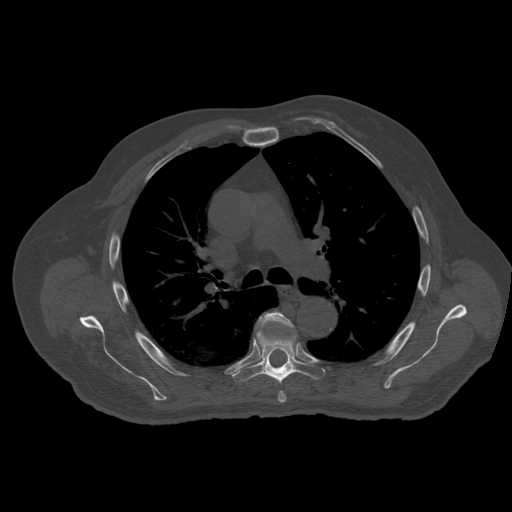
CT including the spine, one axial slice. Position 387 of 399 along the scan axis. Reconstruction kernel STANDARD. 120 kVp. Bone window (W 1800 / L 400 HU). 1.25 mm slice thickness. 512 × 512 image matrix. Patient age 73 years. Case-level facts recorded for this patient, not image findings: primary cancer: prostate; vertebrae with lytic lesions (as recorded): L2.
Structures marked on this image (semi-automatic segmentation, software-assisted and operator-edited):
- T5 vertebra: bounding box <260,312,293,403> (left, top, right, bottom; pixels)
- T6 vertebra: <234,326,325,384>